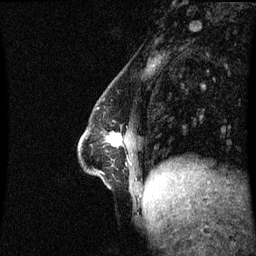
Breast MRI (dynamic contrast-enhanced), one sagittal slice; slice 23 of 60 in the series (ordered by position); dynamic contrast-enhanced series, image 2 of 3 at this slice position (ordered by acquisition); 1.5 T; TE 4.2 ms, TR 8.9 ms; 256 × 256 image matrix, field of view 210 × 210 mm. Patient: female, 47 years. From the clinical record (not read from this slice): setting: breast cancer imaged before/during neoadjuvant chemotherapy; receptor status: HR-positive, HER2-negative.
Outlined on this slice (semi-automatic segmentation, software-assisted and operator-edited):
- analysis volume of interest (the breast-tissue region the enhancement analysis was run in; not a lesion): bounding box [x1, y1, x2, y2] px = [79, 133, 142, 196]
- tumour enhancement mask (voxels above the 70 % enhancement threshold inside the analysis volume of interest): [110, 135, 121, 146]